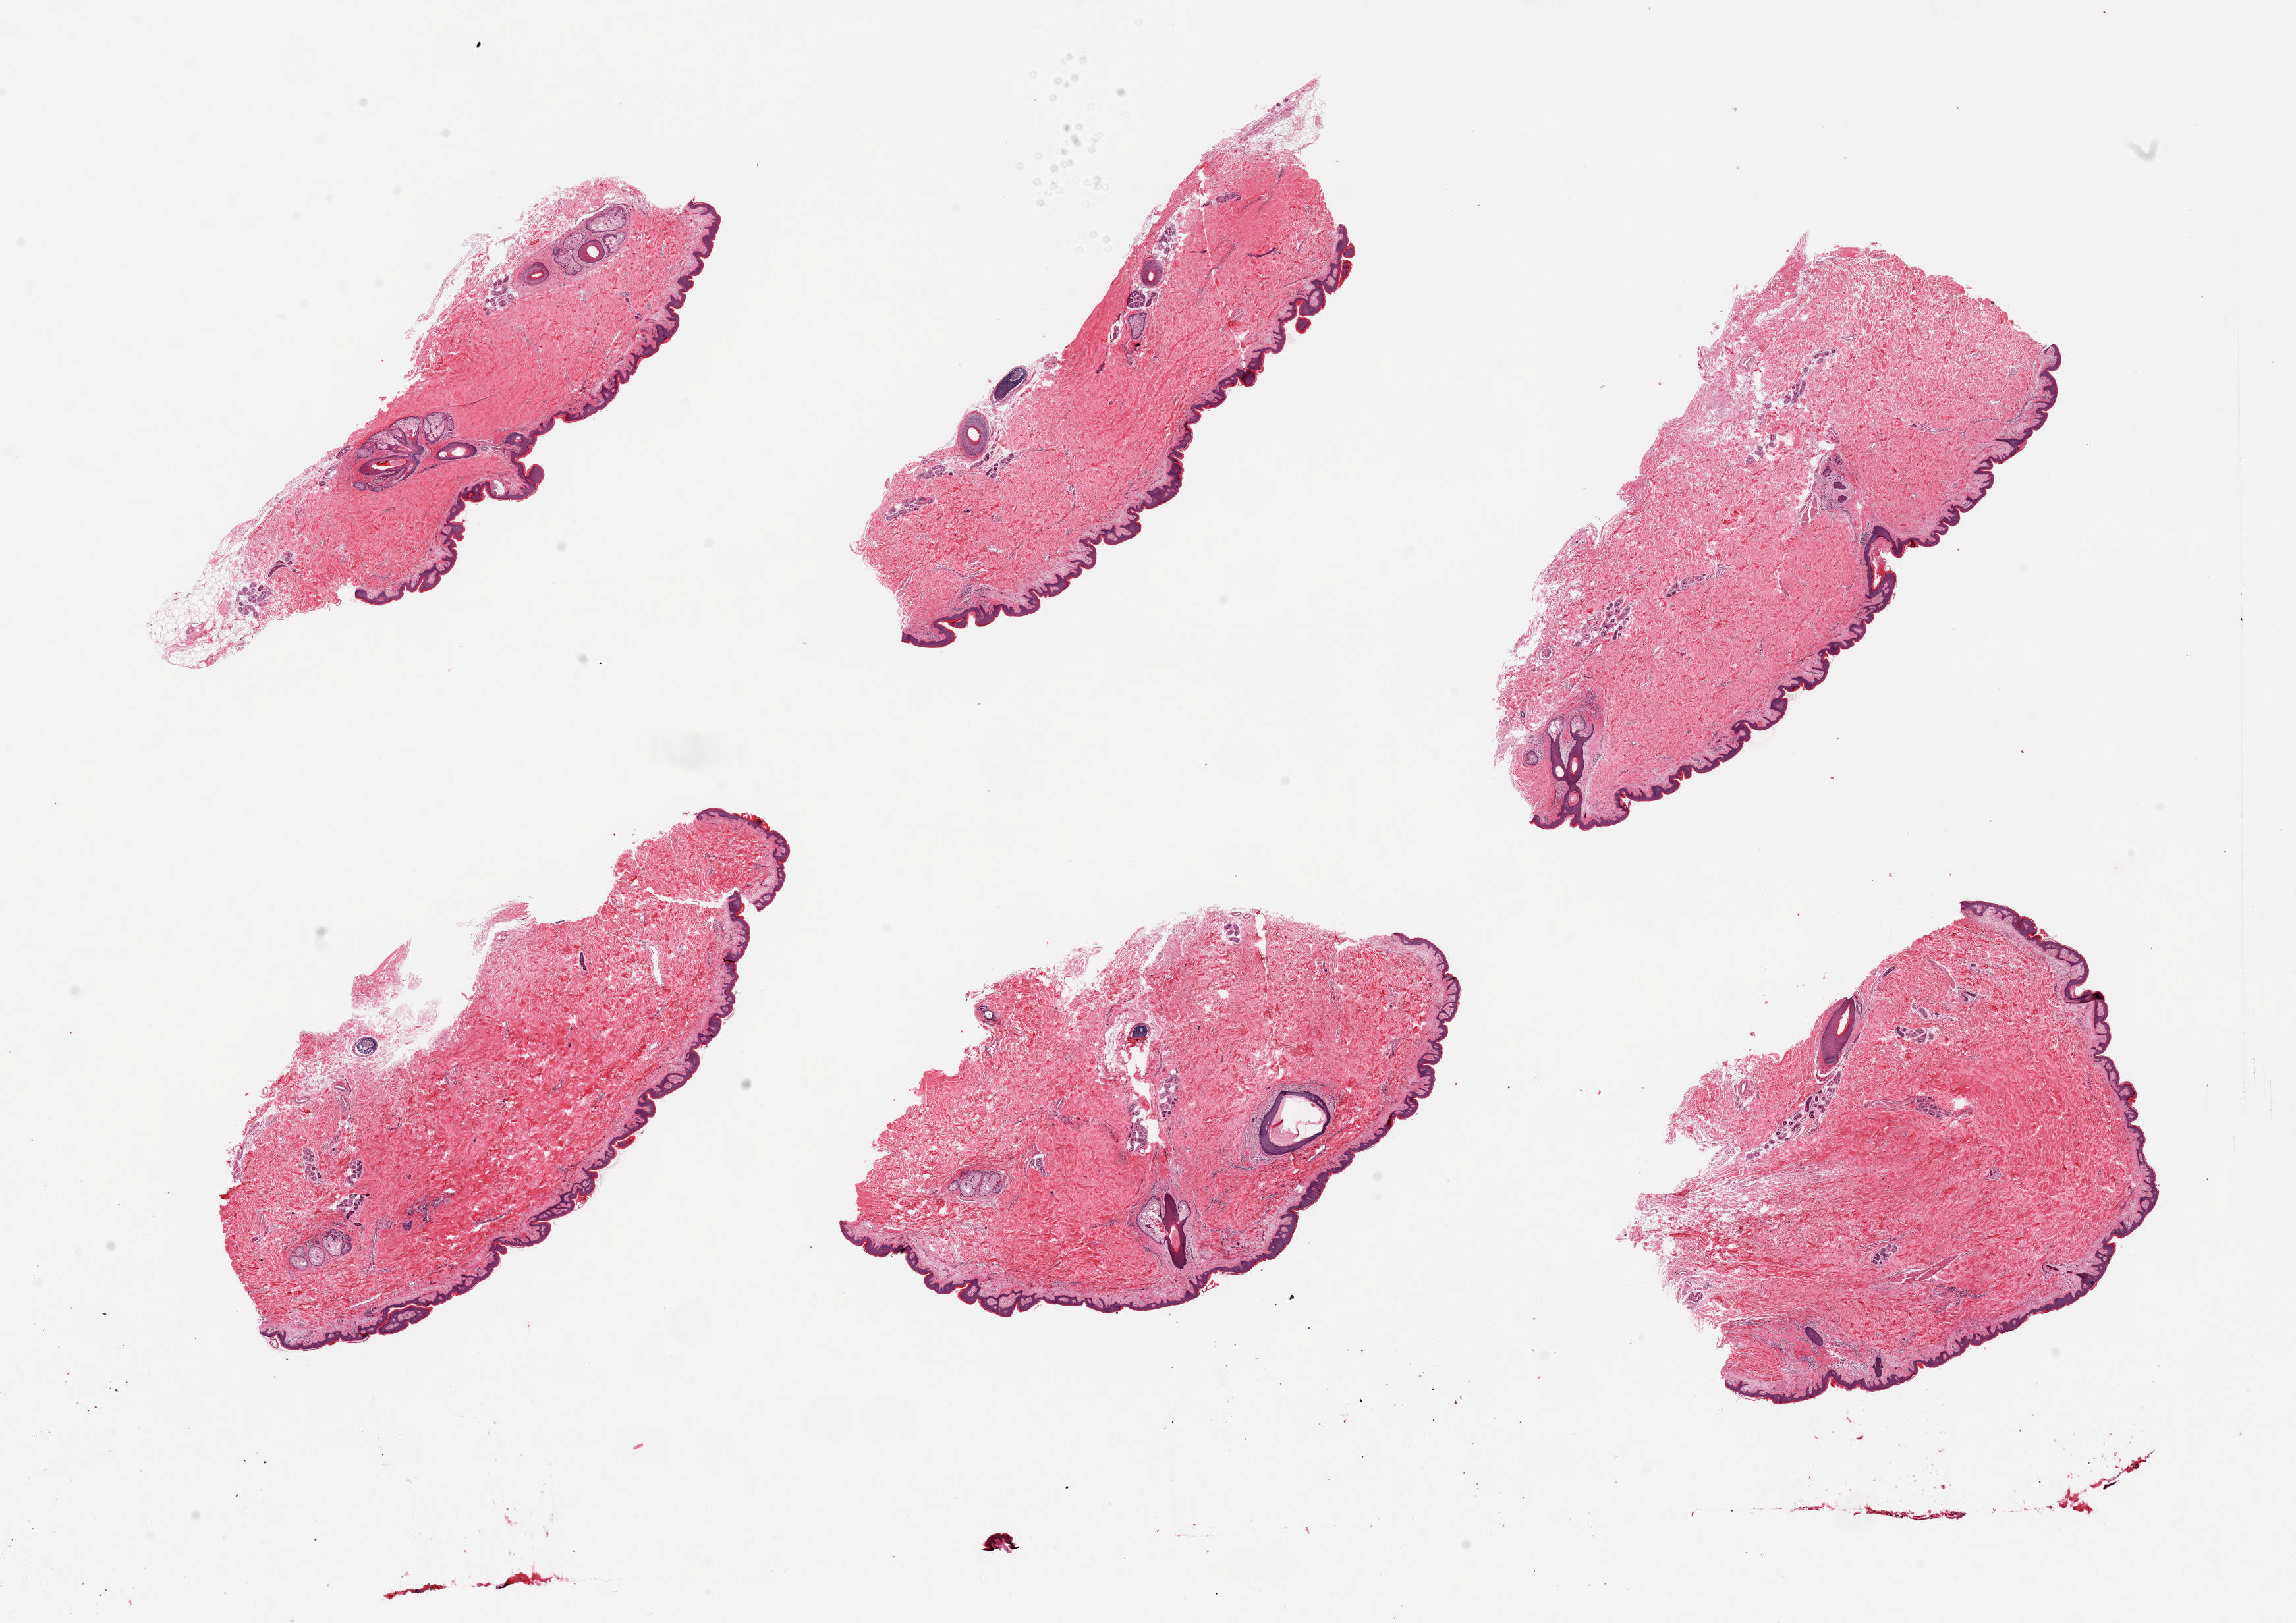
Hematoxylin and eosin (H&E) whole-slide image — low-resolution overview of the scanned area, about 27.6 x 19.5 mm (slide scanned at 20x), PAXgene-fixed paraffin-embedded (PFPE) section, section of skin of suprapubic region (target tissue), tissue donor sample. Male donor.
Review note (as recorded): 6 pieces; hair bearing skin with one small hair follicle retention cyst; essentially well trimmed.